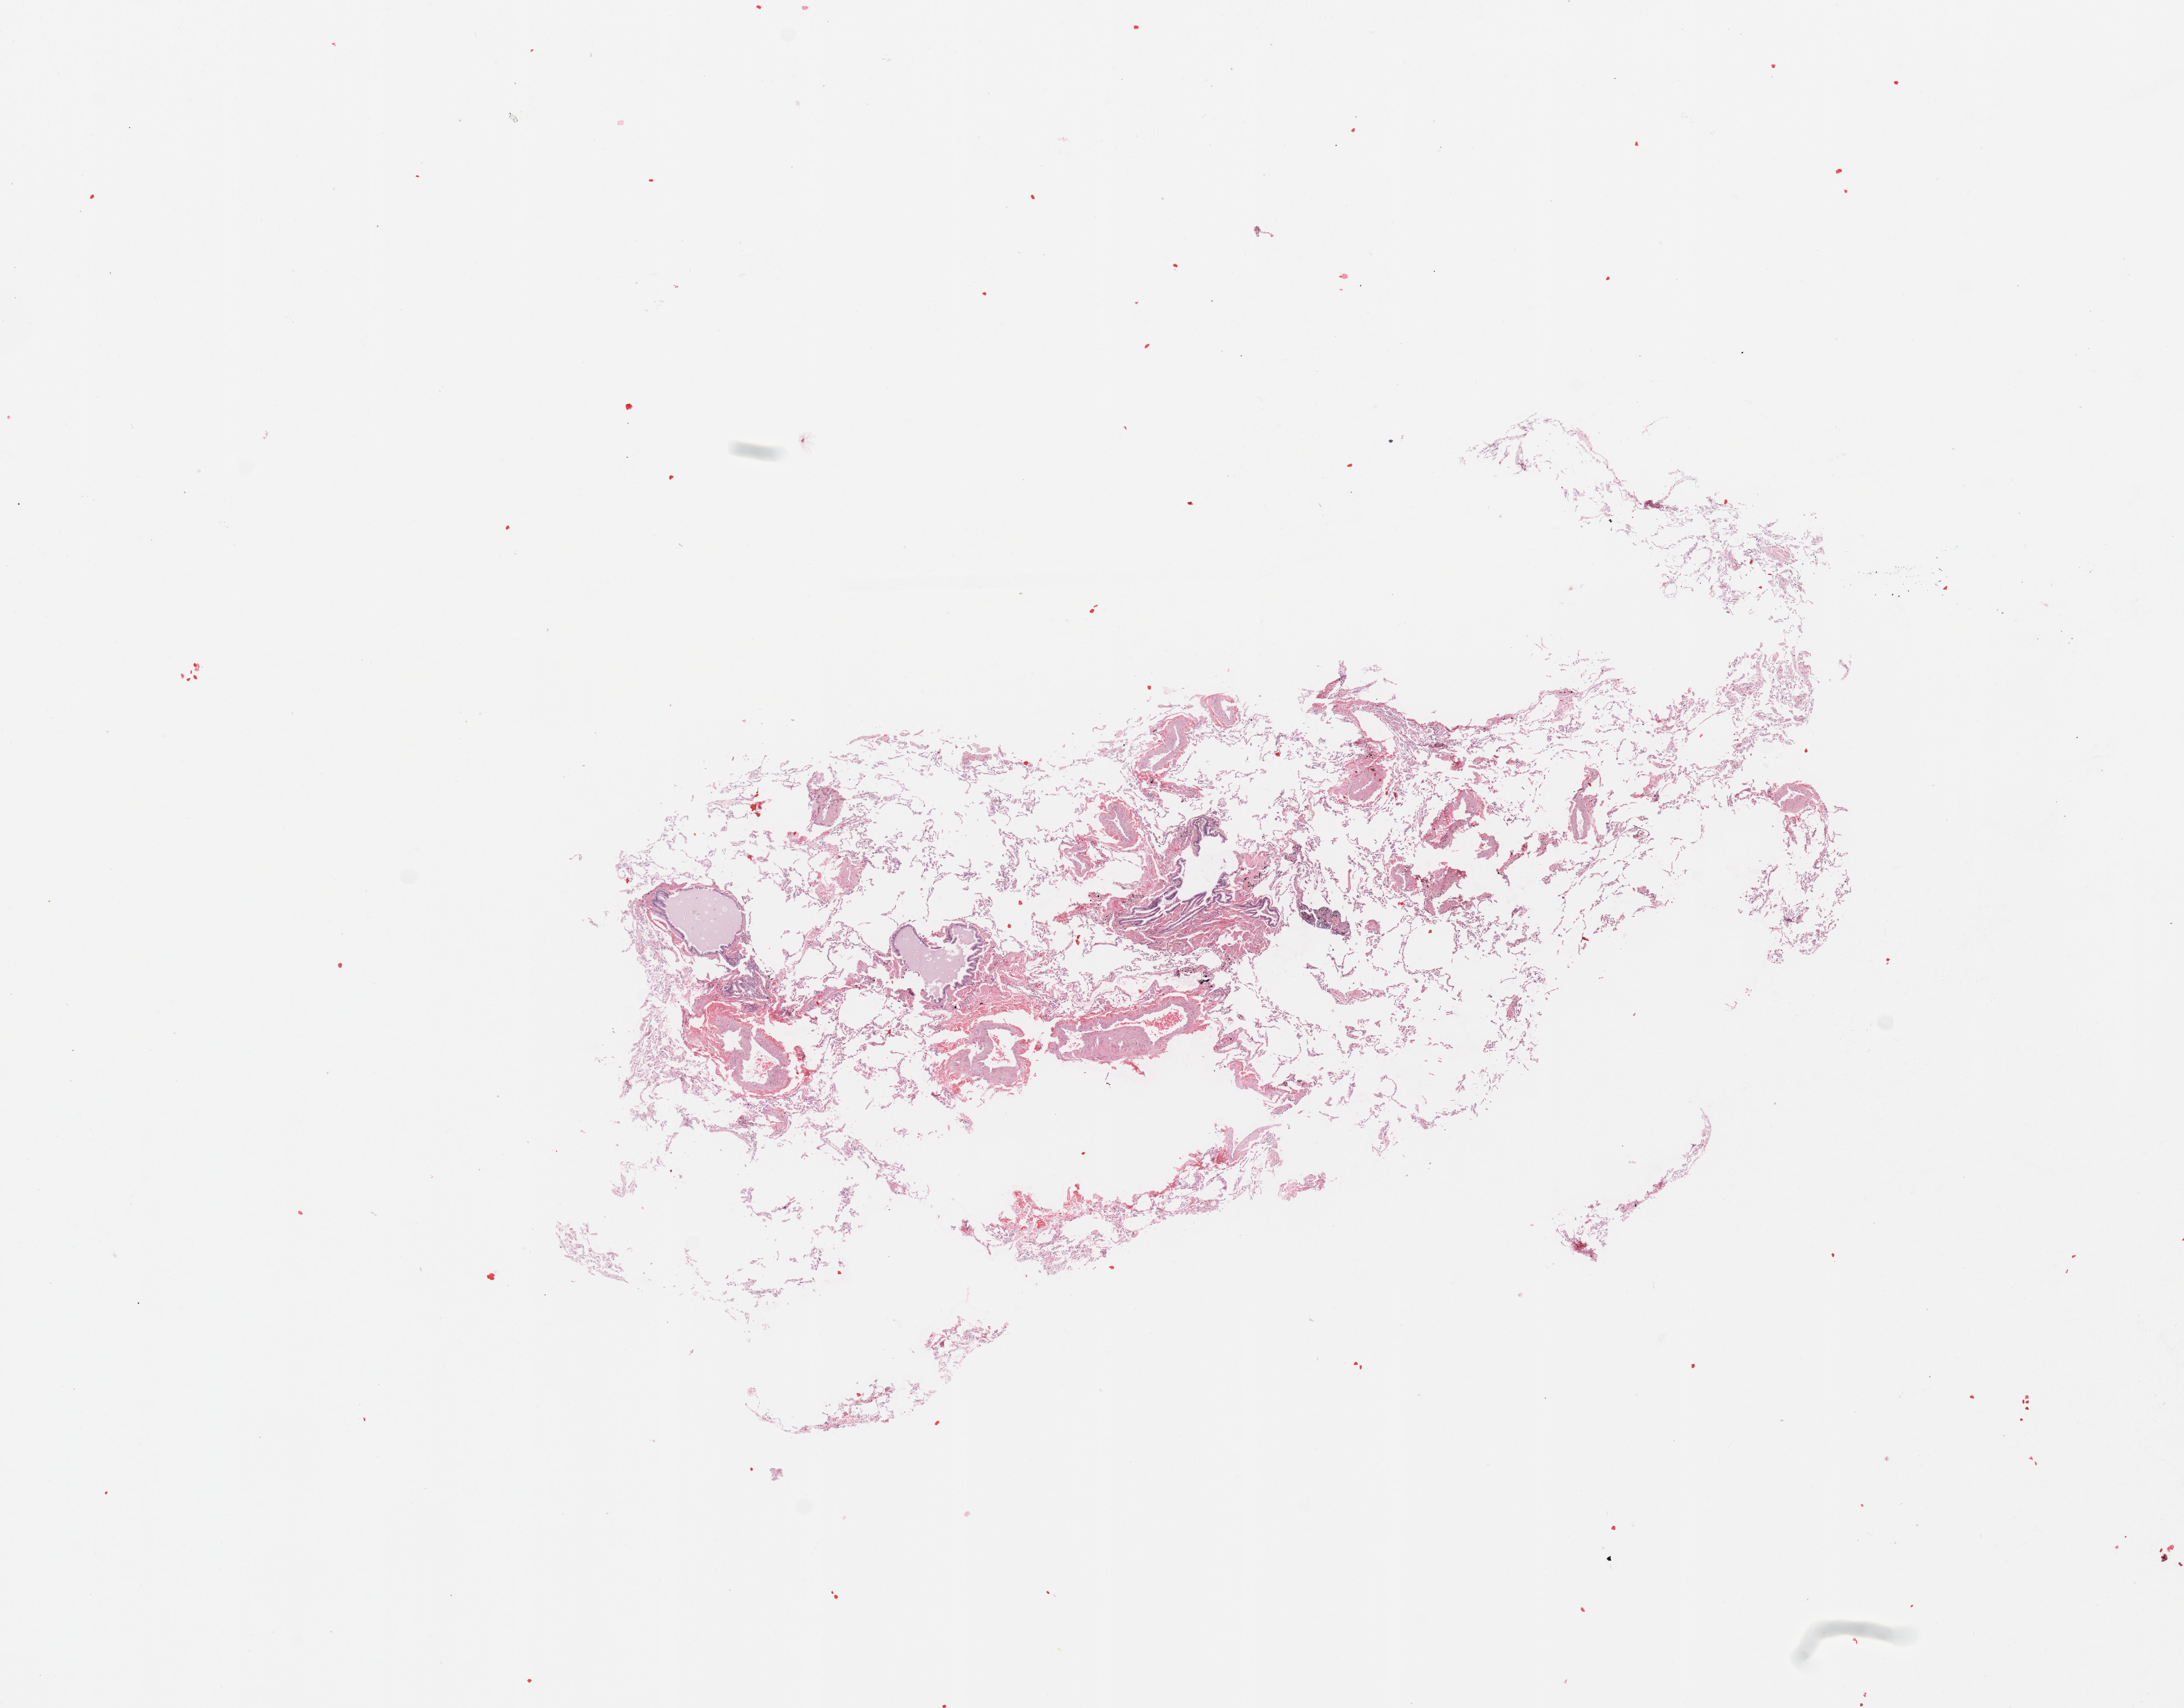
Whole-slide histology image, Hematoxylin and eosin (H&E) stained — a low-resolution overview of the entire scanned area, about 14.8 x 11.6 mm (from a 20x scan), normal (non-tumour) tissue sample, sampled site: lung. Male, 68 y/o.
This section: normal (non-tumour) tissue from the same patient. Patient diagnosis: Squamous cell carcinoma, NOS.